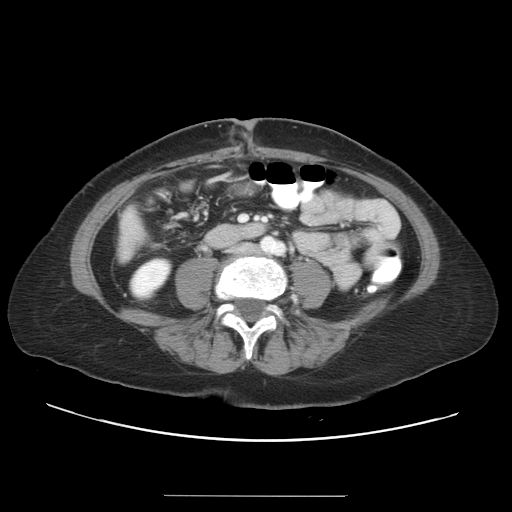
Contrast-enhanced abdominal CT, one axial slice; slice 2 of 34 in the series (ordered by position); intravenous contrast given; soft-tissue window (W 400 / L 40 HU); 5 mm slice thickness; 512 × 512 image matrix, field of view 382 × 382 mm. Female patient, age 69 years. Case-level facts recorded for this patient, not image findings: diagnosis: colorectal cancer liver metastases, imaged before liver resection; multiple liver metastases: yes; largest metastasis: 1.4 cm; disease in both lobes: yes.
Annotated regions visible in this slice (manually delineated by an expert):
- liver: bounding box (x1, y1, x2, y2) in pixels: (121, 210, 146, 254)
- planned liver remnant (the part of the liver to remain after resection): (121, 228, 146, 254)
- portal vein (with intrahepatic branches): (240, 216, 246, 221)